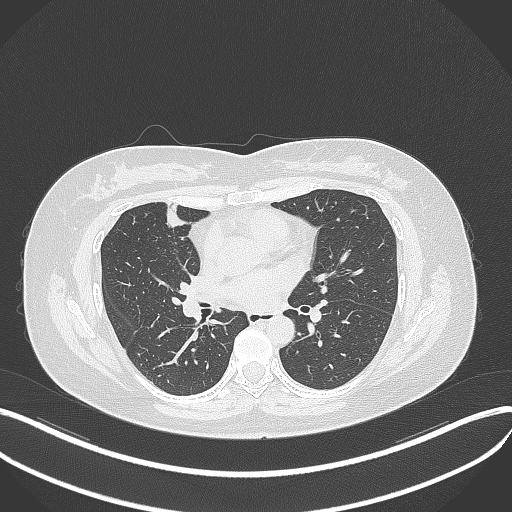
Chest CT, one axial slice; reconstruction kernel B70f; 120 kVp; lung window (W 1500 / L -600 HU); 1 mm slice thickness; 512 × 512 image matrix. Female patient, age 42 years. Case-level facts recorded for this patient, not image findings: clinical TNM (as recorded): T1b N0 M0.
Annotated regions visible in this slice (bounding box drawn by a radiologist):
- lung tumour (recorded histology: adenocarcinoma): box from (x=161, y=198) to (x=190, y=232) px